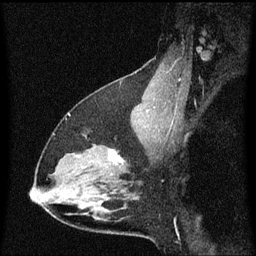
Breast MRI (dynamic contrast-enhanced), one sagittal slice; slice 41 of 60 in the series (ordered by position); dynamic contrast-enhanced series, image 2 of 3 at this slice position (ordered by acquisition); 1.5 T; TE 4.2 ms, TR 8.4 ms; 256 × 256 image matrix. Patient: female, 38 years. From the clinical record (not read from this slice): setting: breast cancer imaged before/during neoadjuvant chemotherapy; receptor status: HR-positive, HER2-negative.
Annotated regions visible in this slice (semi-automatically segmented with operator editing):
- analysis volume of interest (the breast-tissue region the enhancement analysis was run in; not a lesion): bounding box (x1, y1, x2, y2) in pixels: (94, 144, 141, 185)
- tumour enhancement mask (voxels above the 70 % enhancement threshold inside the analysis volume of interest): (109, 150, 124, 163)